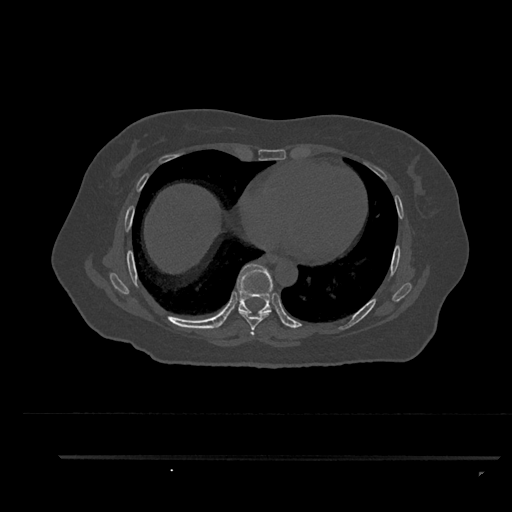
CT including the spine, one axial slice; slice 486 of 797 in the series (ordered by position); reconstruction kernel Br40s/3; 120 kVp; bone window (W 1800 / L 400 HU); 0.5 mm slice thickness; 512 × 512 image matrix, field of view 408 × 408 mm. Female patient, age 44 years. Case-level facts recorded for this patient, not image findings: primary cancer: renal.
Outlined on this slice (semi-automatic segmentation, software-assisted and operator-edited):
- T7 vertebra: bounding box <239,311,272,336> (left, top, right, bottom; pixels)
- T8 vertebra: <236,263,281,320>